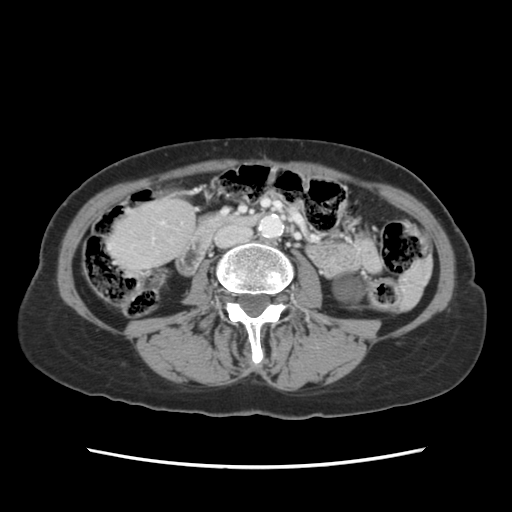
Contrast-enhanced abdominal CT, one axial slice; position 18 of 120 along the scan axis; intravenous contrast given; soft-tissue window (W 400 / L 40 HU); 2.5 mm slice thickness; 512 × 512 image matrix. Female patient, age 70 years. Case-level facts recorded for this patient, not image findings: diagnosis: colorectal cancer liver metastases, imaged before liver resection; multiple liver metastases: no; largest metastasis: 2.5 cm; disease in both lobes: no.
Annotated regions visible in this slice (manually delineated by an expert):
- liver: bounding box [x1, y1, x2, y2] px = [112, 200, 191, 269]
- planned liver remnant (the part of the liver to remain after resection): [112, 200, 191, 268]